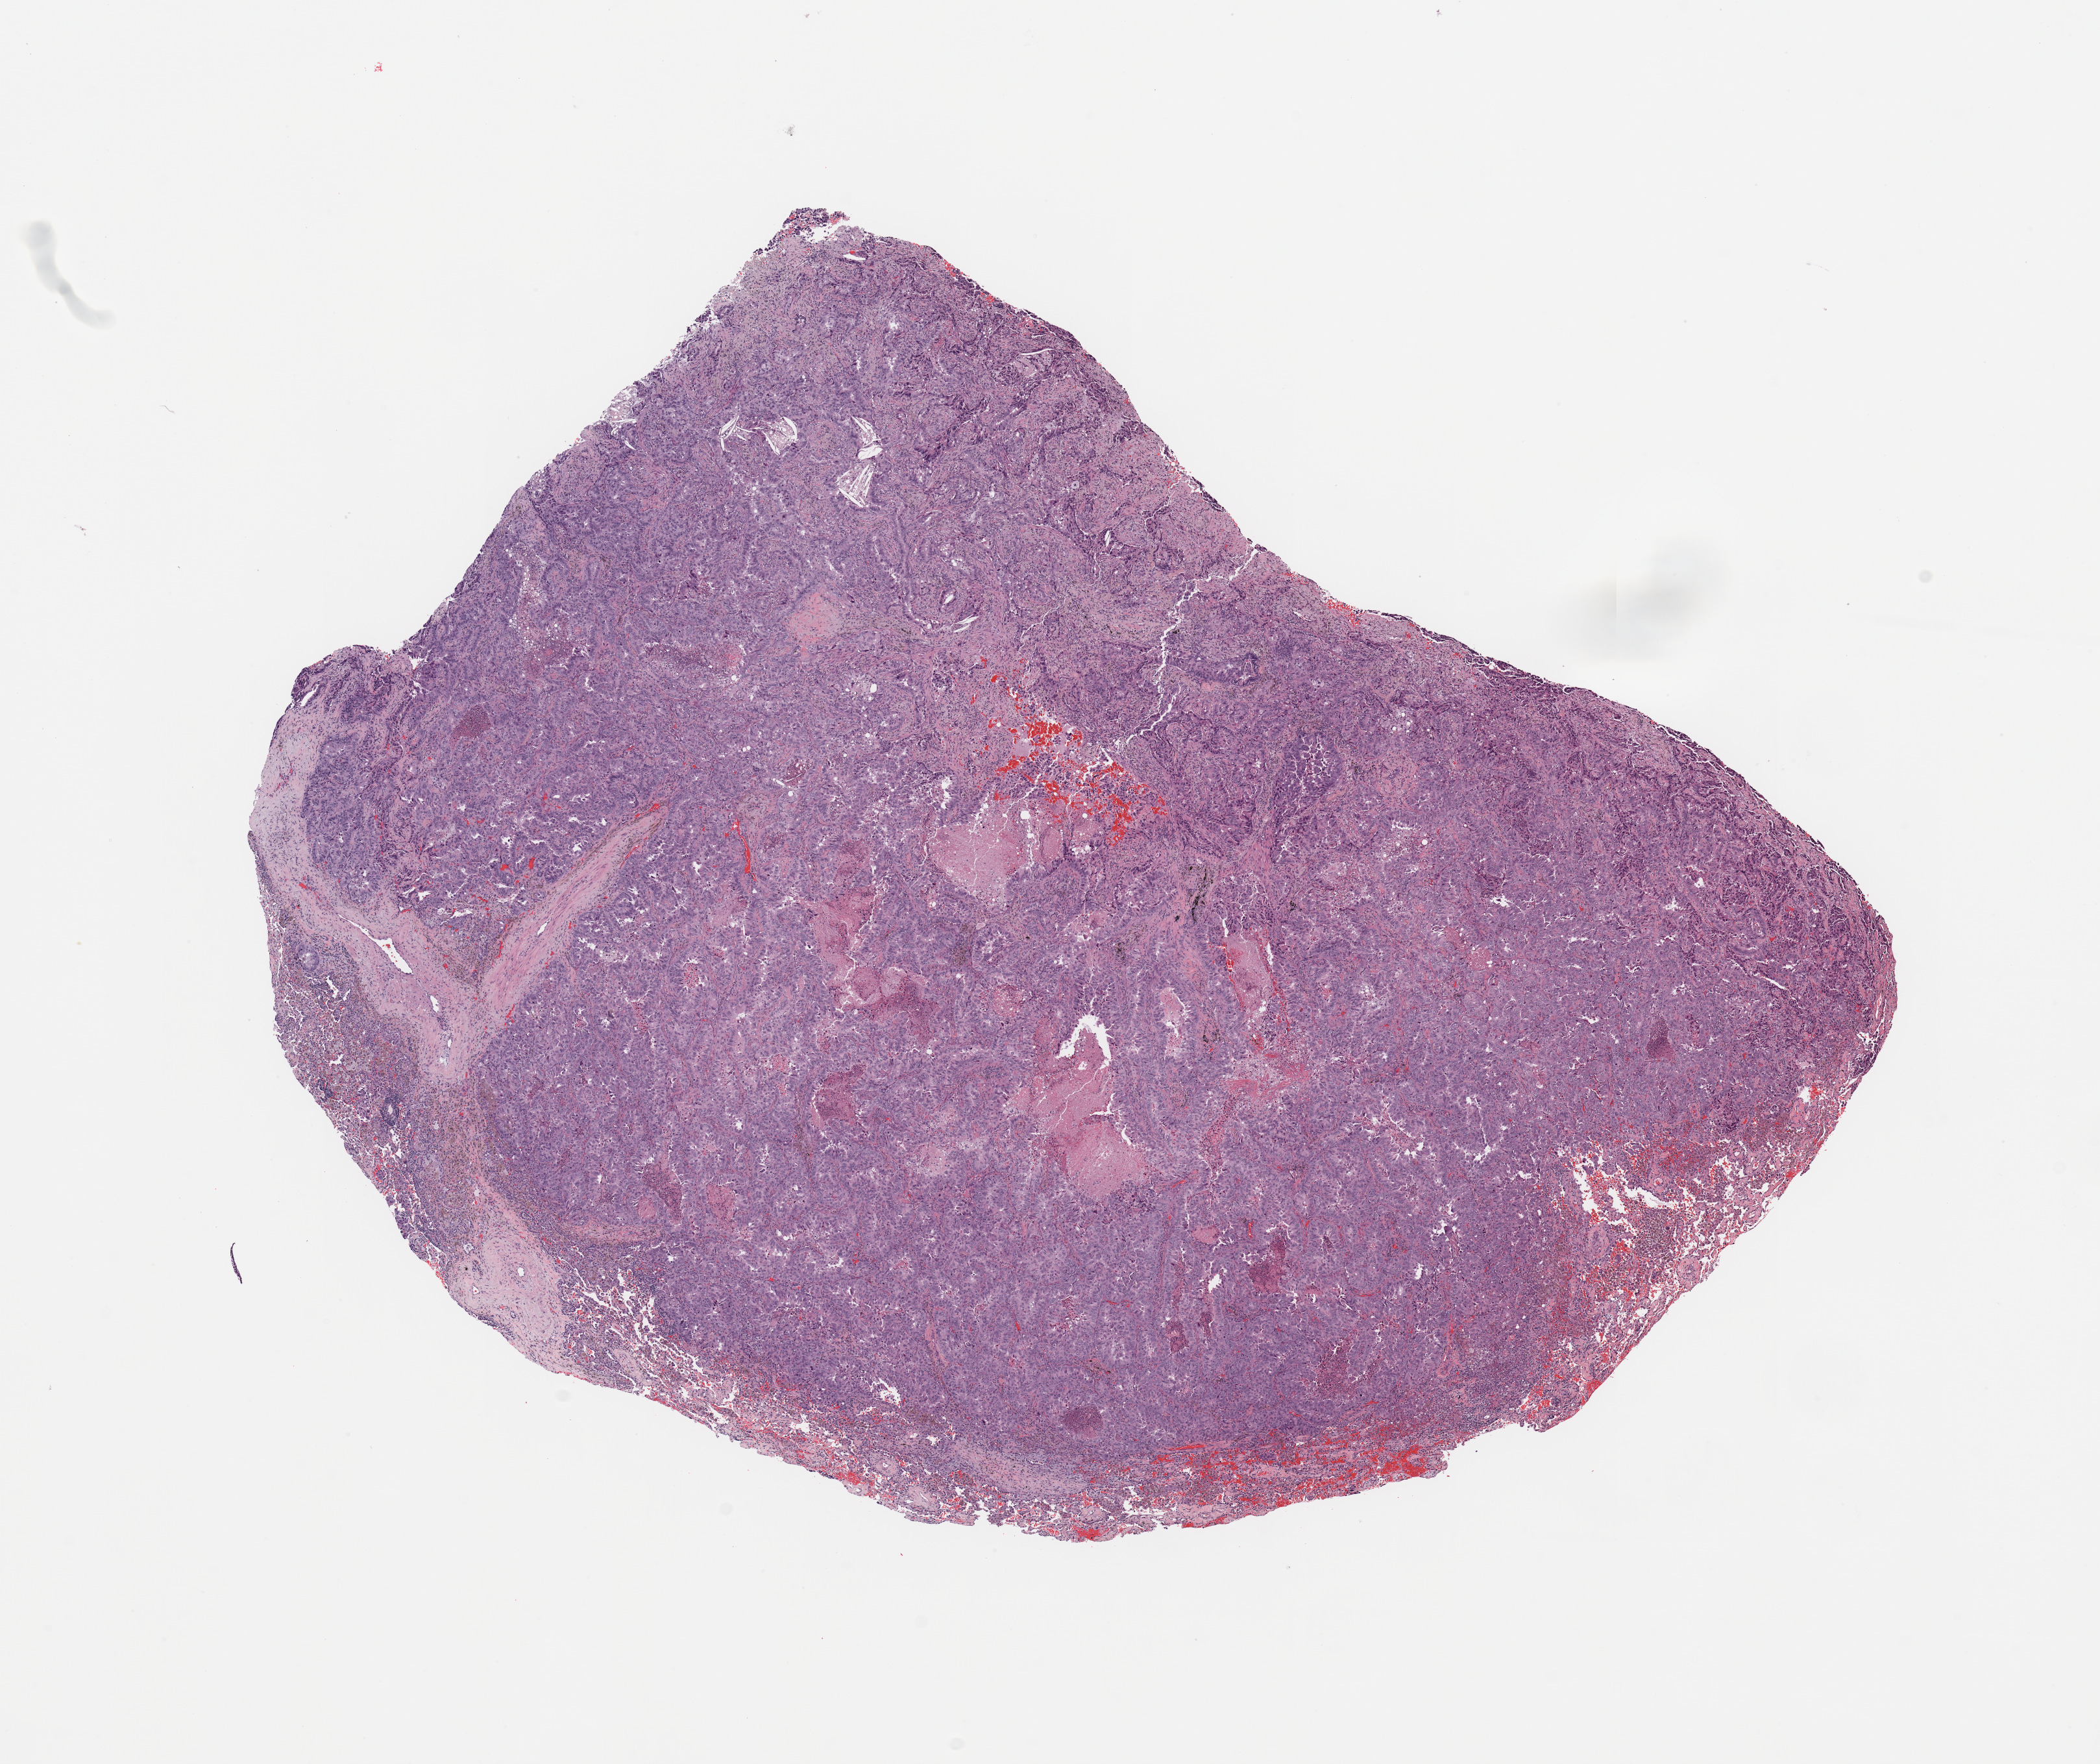
Whole-slide histology image, H&E — shown as a low-resolution overview of the whole scanned area (about 12.8 x 10.7 mm, from a 20x scan); tumour tissue sample, sampled site: lung. 62-year-old female patient. Histologic grade: G3 (poorly differentiated). Slide review estimates, as recorded: tumour nuclei 80%, necrosis 5%.
- primary tumour site (as recorded): right lower lobe
- AJCC pathologic stage: IIB
- diagnosis: Adenocarcinoma, NOS